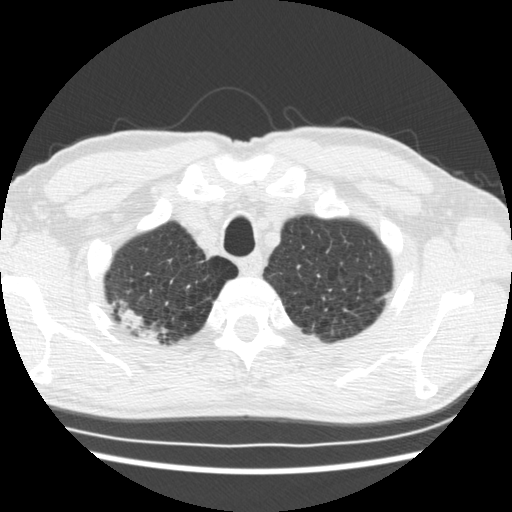
Low-dose screening chest CT, one axial slice; slice 159 of 183 in the series (ordered by position); lung window (W 1500 / L -600 HU); 512 × 512 image matrix.
Outlined on this slice (outlined manually by an expert reader):
- lesion 1 (tumor, upper lobe of right lung): bounding box (x1, y1, x2, y2) in pixels: (121, 307, 159, 342)